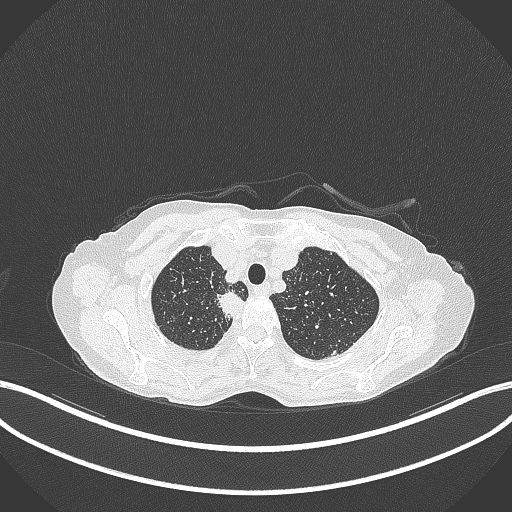
Chest CT, one axial slice; position 318 of 403 along the scan axis; reconstruction kernel B70f; 120 kVp; lung window (W 1500 / L -600 HU); 512 × 512 image matrix, field of view 400 × 400 mm. Female patient, age 75 years. From the clinical record (not read from this slice): clinical TNM (as recorded): T1c N1 M1.
Structures marked on this image (rectangle marked by the reading radiologist):
- lung tumour (recorded histology: adenocarcinoma): bounding box <212,289,248,322> (left, top, right, bottom; pixels)